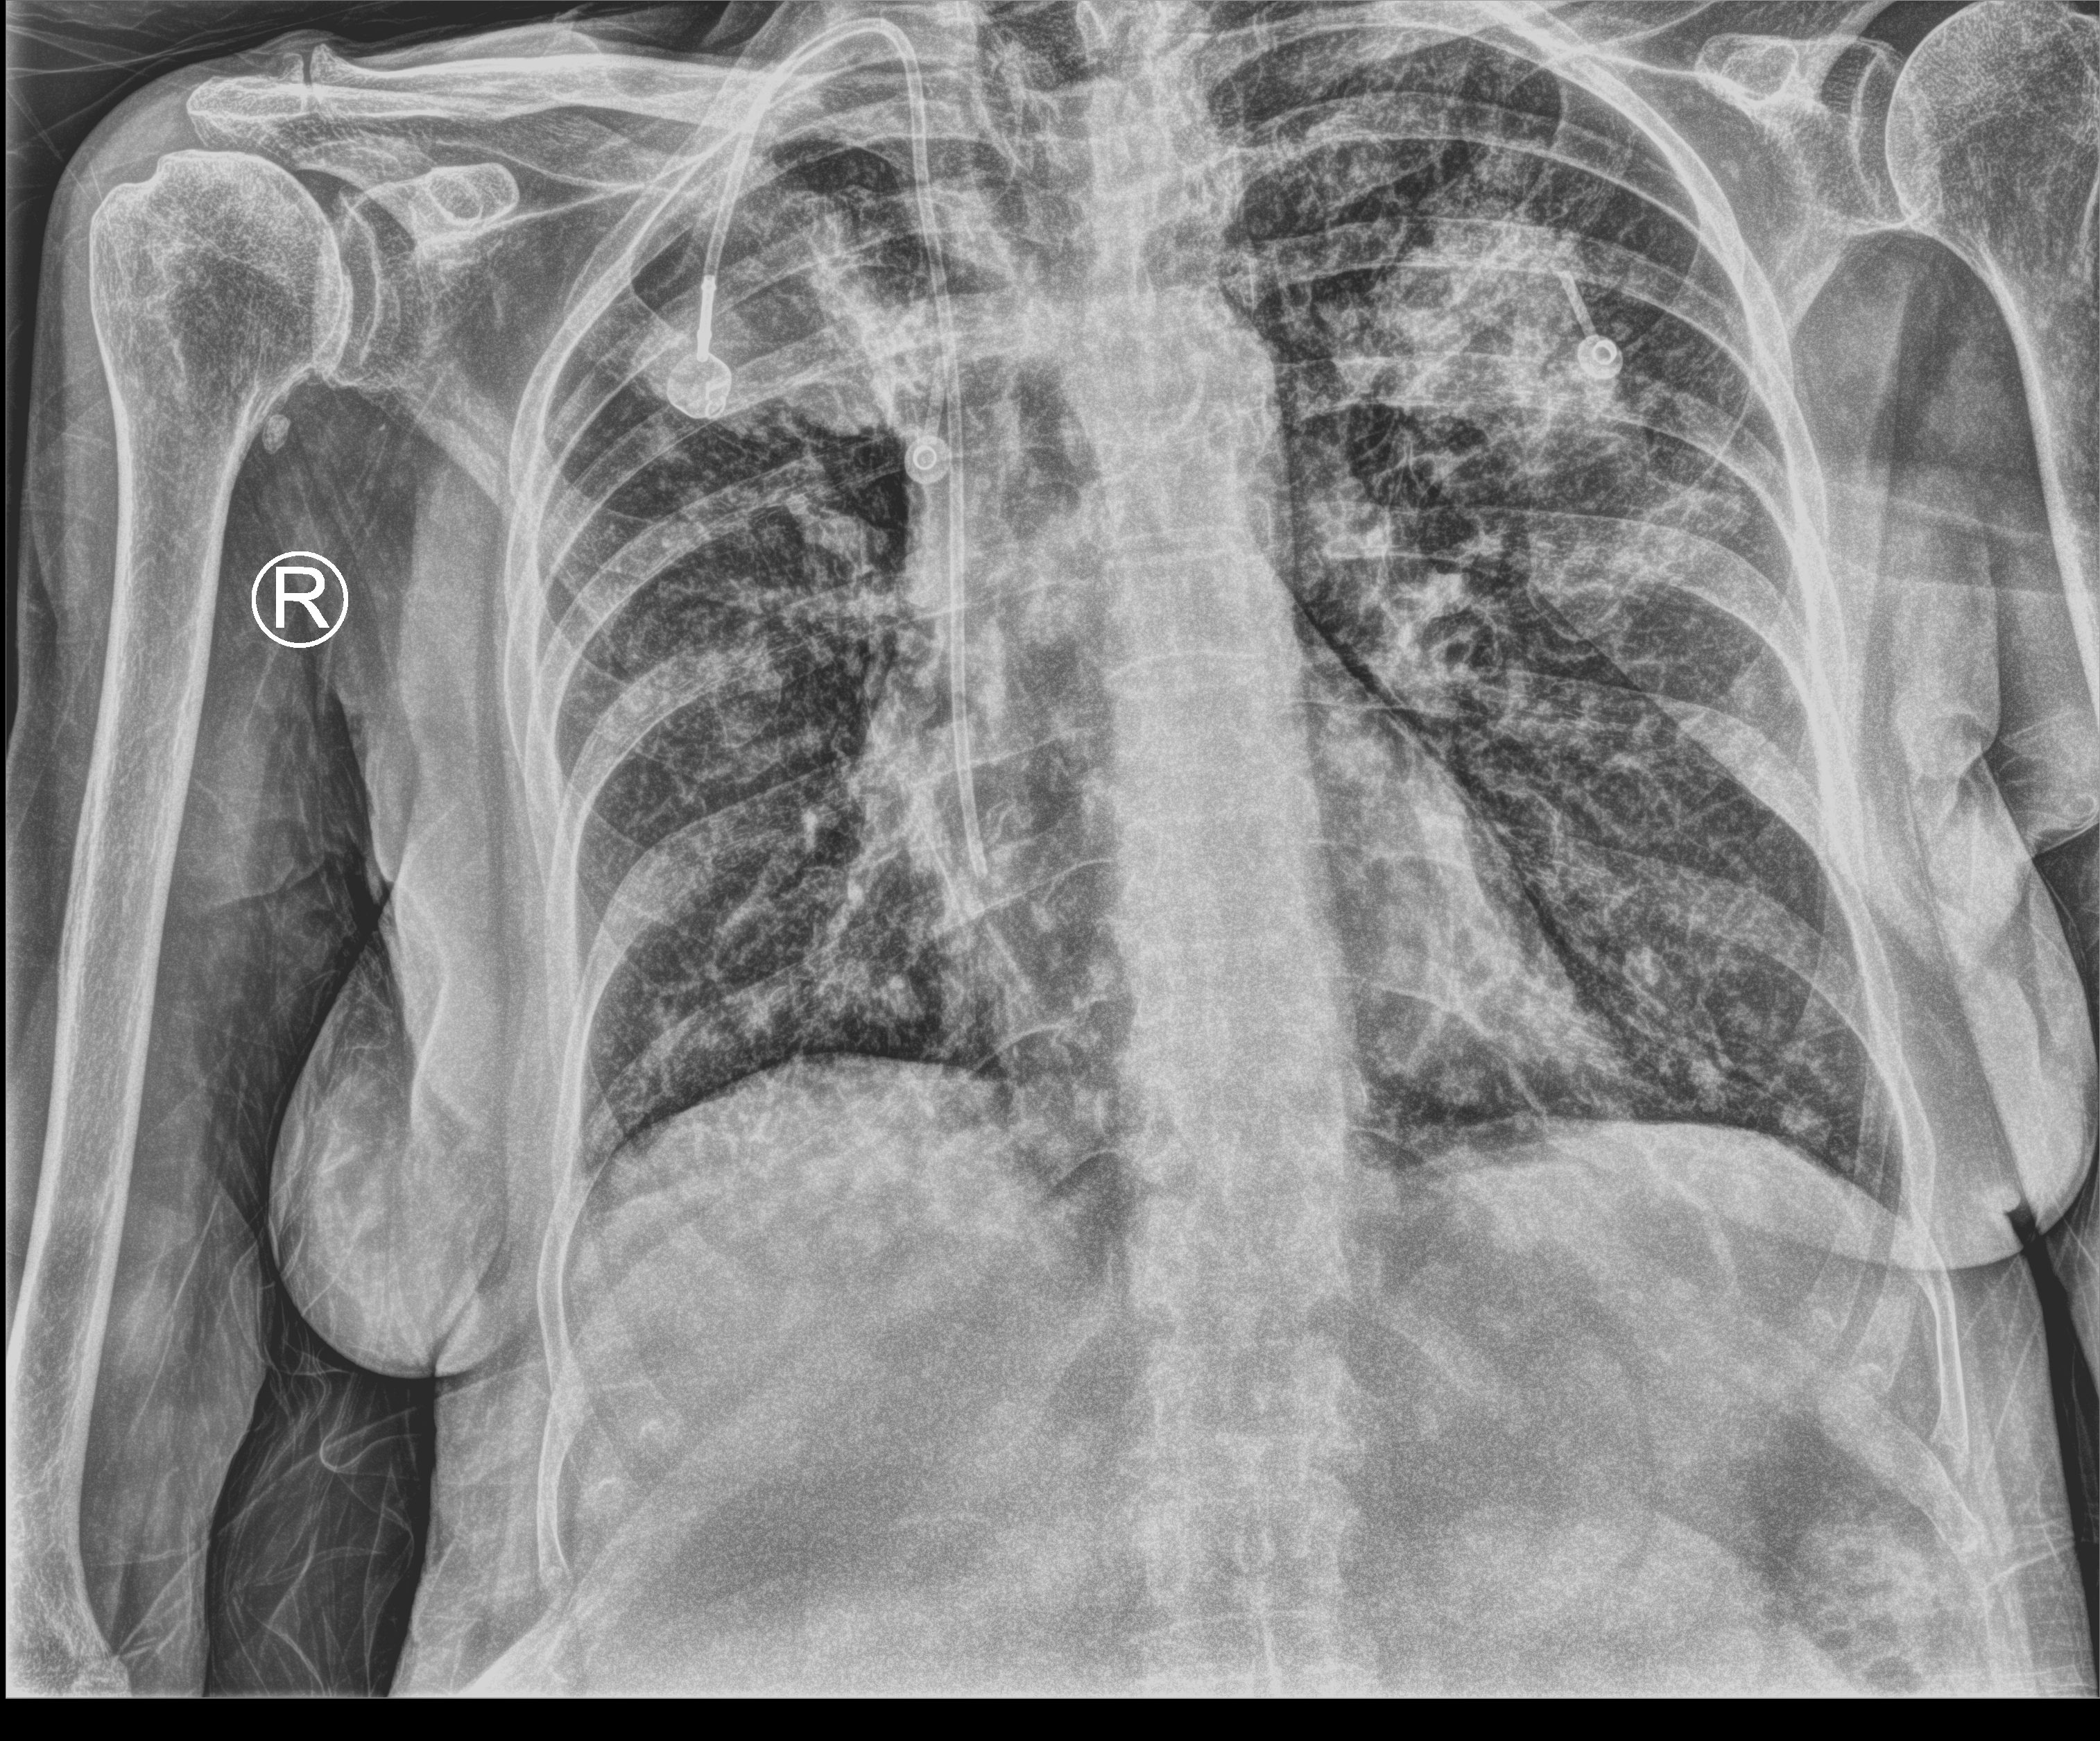
Bedside chest radiograph (computed radiography); anteroposterior (AP) projection. Patient hospitalised with COVID-19; female, aged 60–74 years.
Admission-level facts for this patient (not findings on this image; timing relative to this image not recorded): length of hospital stay: 8 days; admitted to intensive care during this hospital stay: no.